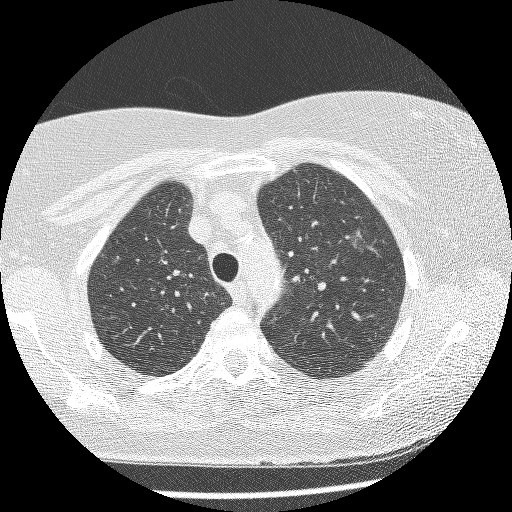
Axial slice from a low-dose chest CT screening exam, first (baseline) screen, lung window (W 1500 / L -600 HU), slice 180 of 241 in the series. Female, age 61 years at enrolment. Current smoker at enrolment.
Lesion marked by an expert reader, bounding box [x1, y1, x2, y2] px = [329, 218, 382, 267]. The screening reader recorded 4 non-calcified nodules or masses ≥4 mm on this exam (right lower lobe, right middle lobe, right lower lobe, left upper lobe); which of them this box marks is not recorded. Official screen result: positive, change unspecified: nodule(s) >= 4 mm or enlarging nodule(s), mass(es), or other non-specific abnormalities suspicious for lung cancer. Lung cancer was diagnosed 111 days after this screen: bronchiolo-alveolar adenocarcinoma, NOS, left upper lobe, stage IV (AJCC 6th edition), 10 mm at pathology.